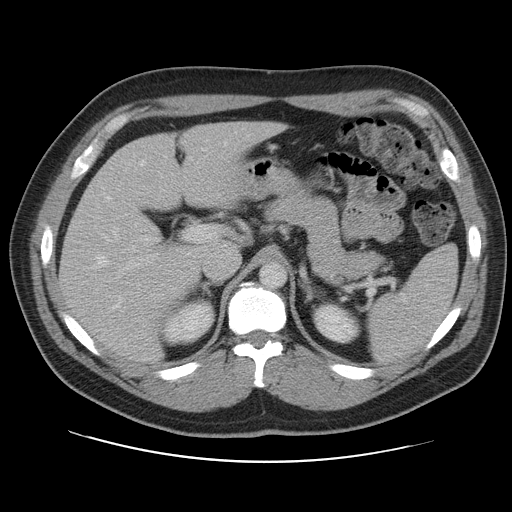
Contrast-enhanced abdominal CT, one axial slice; 120 kVp; intravenous contrast given; soft-tissue window (W 400 / L 40 HU); 5 mm slice thickness; 512 × 512 image matrix. Male patient, age 35 years. Case-level facts recorded for this patient, not image findings: diagnosis: colorectal cancer liver metastases, imaged before liver resection; multiple liver metastases: yes.
Annotated regions visible in this slice (manually delineated by an expert):
- hepatic veins: bounding box [x1, y1, x2, y2] px = [92, 141, 227, 309]
- liver: [60, 123, 279, 361]
- planned liver remnant (the part of the liver to remain after resection): [60, 122, 279, 361]
- portal vein (with intrahepatic branches): [107, 160, 208, 298]